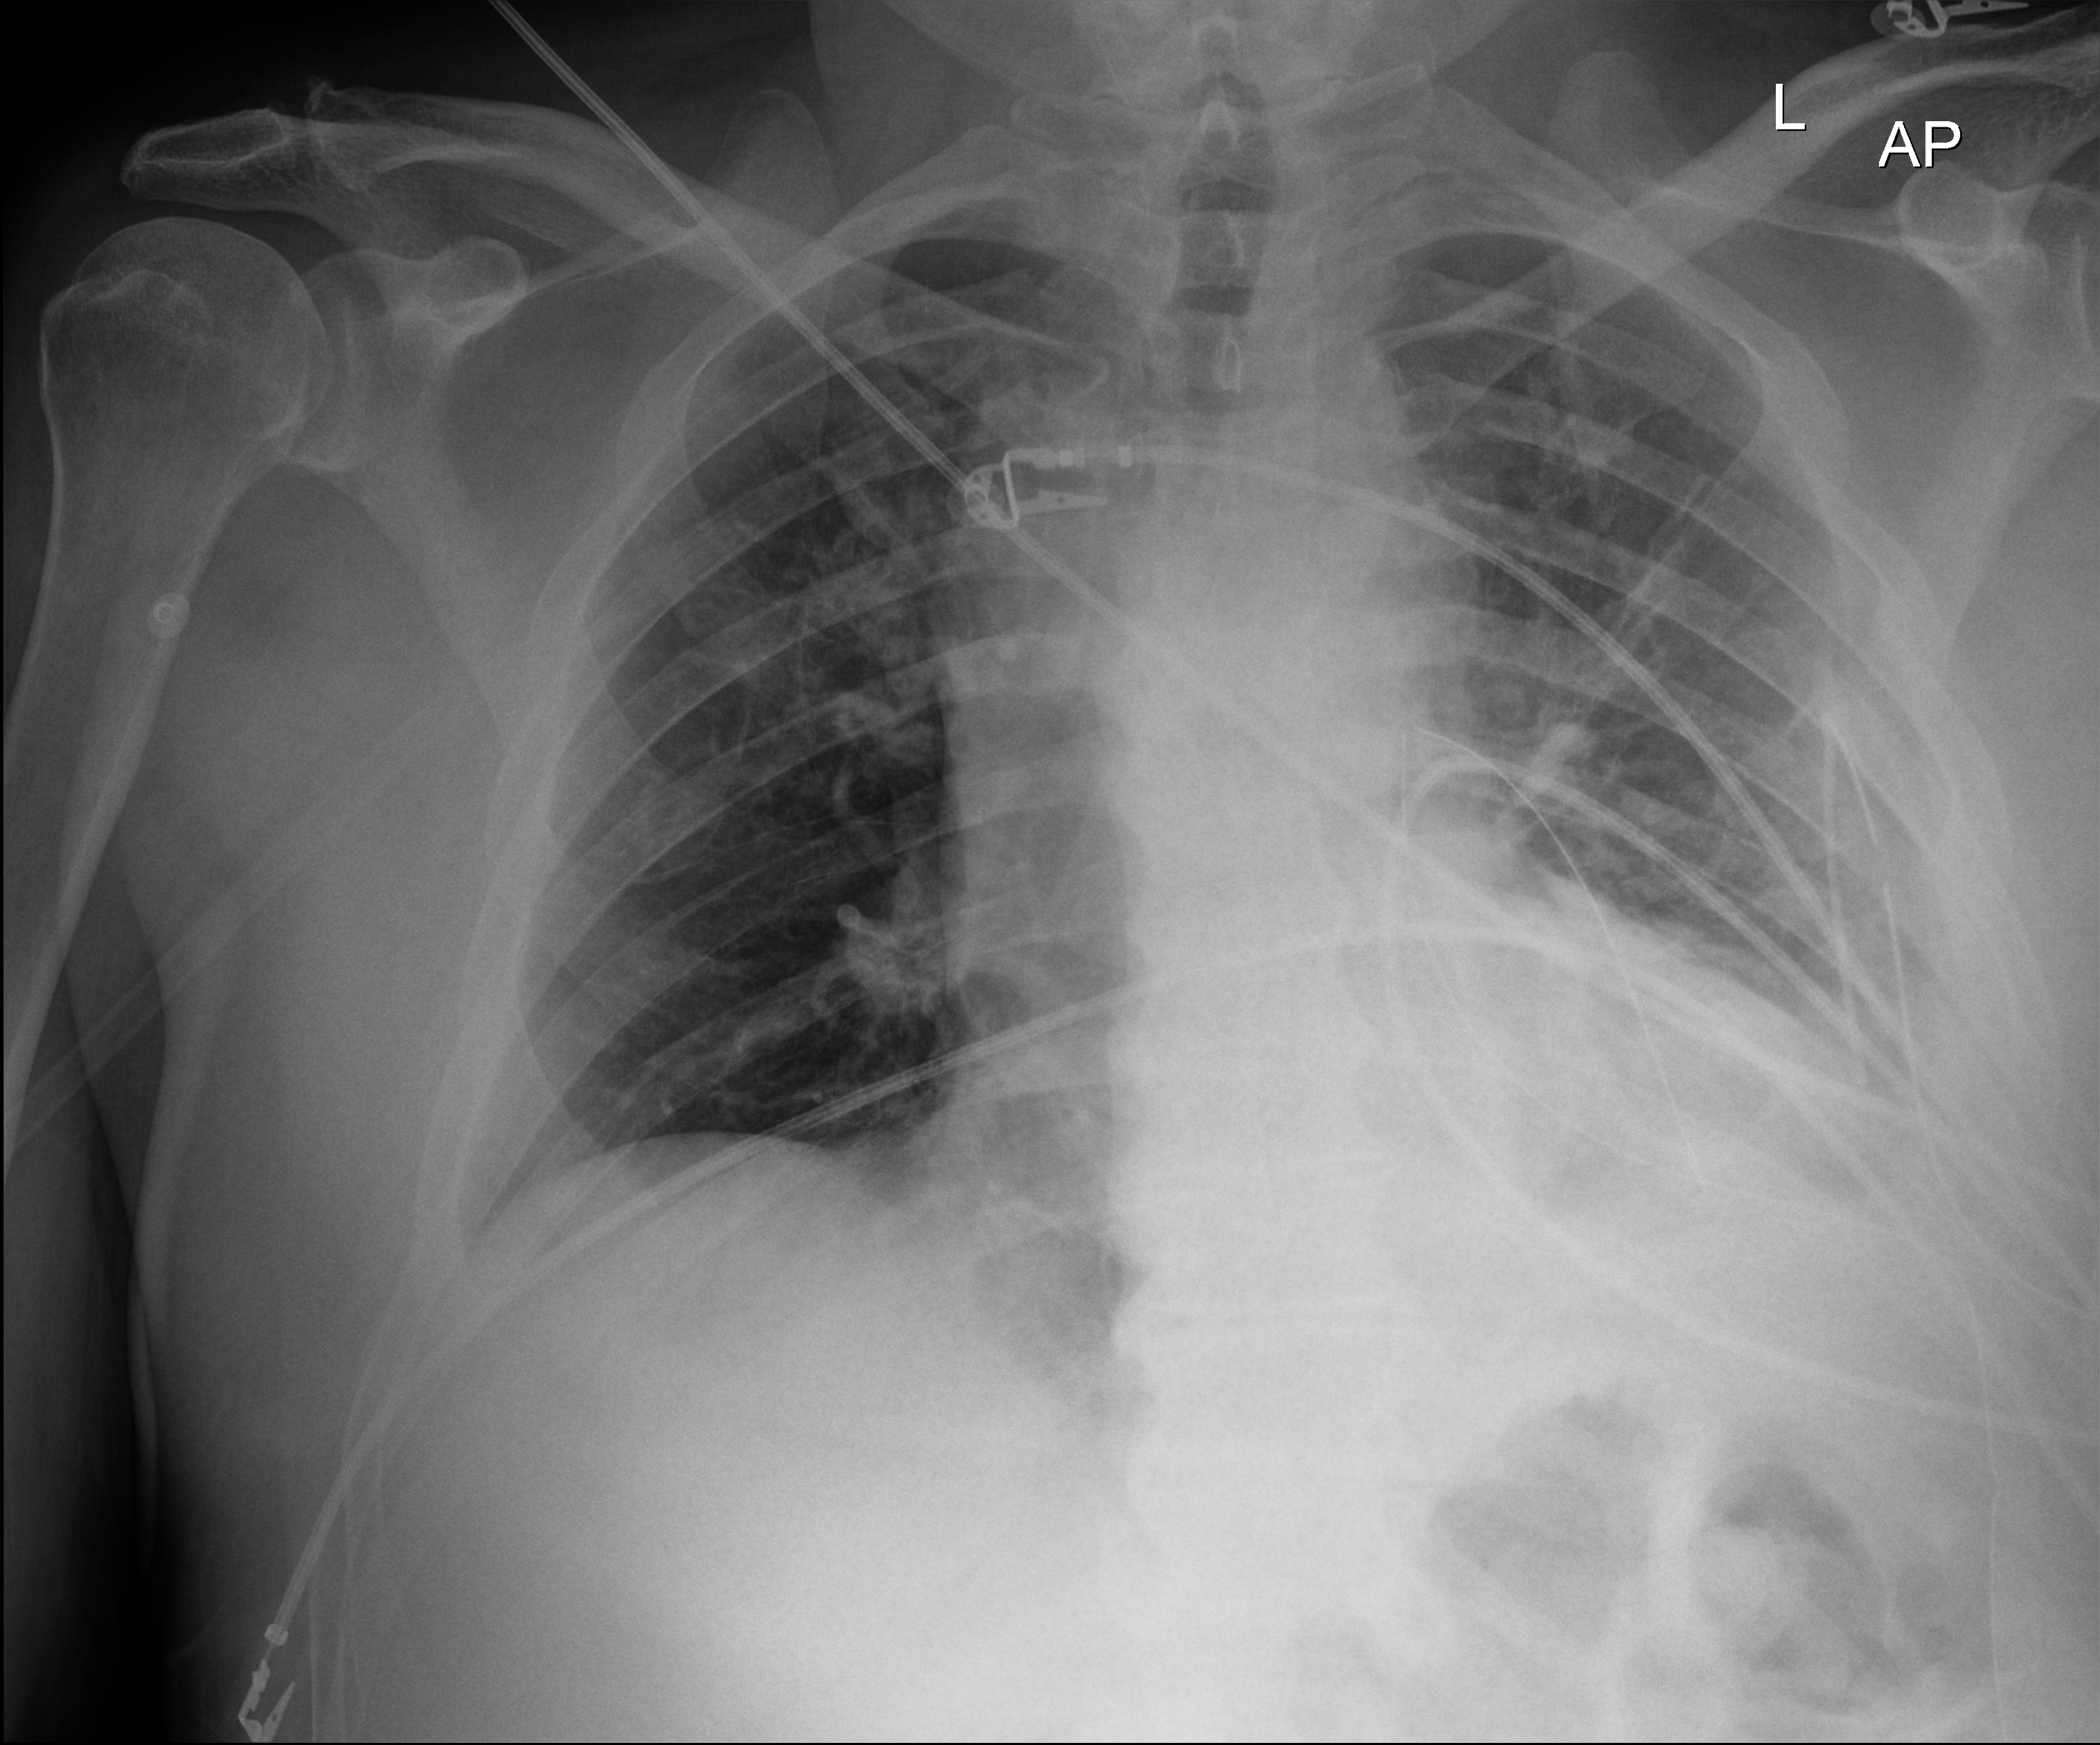
Portable chest radiograph. Male patient hospitalised with COVID-19, age 18–59 years.
Admission-level facts for this patient (not findings on this image; timing relative to this image not recorded): mechanically ventilated during this hospital stay: no.